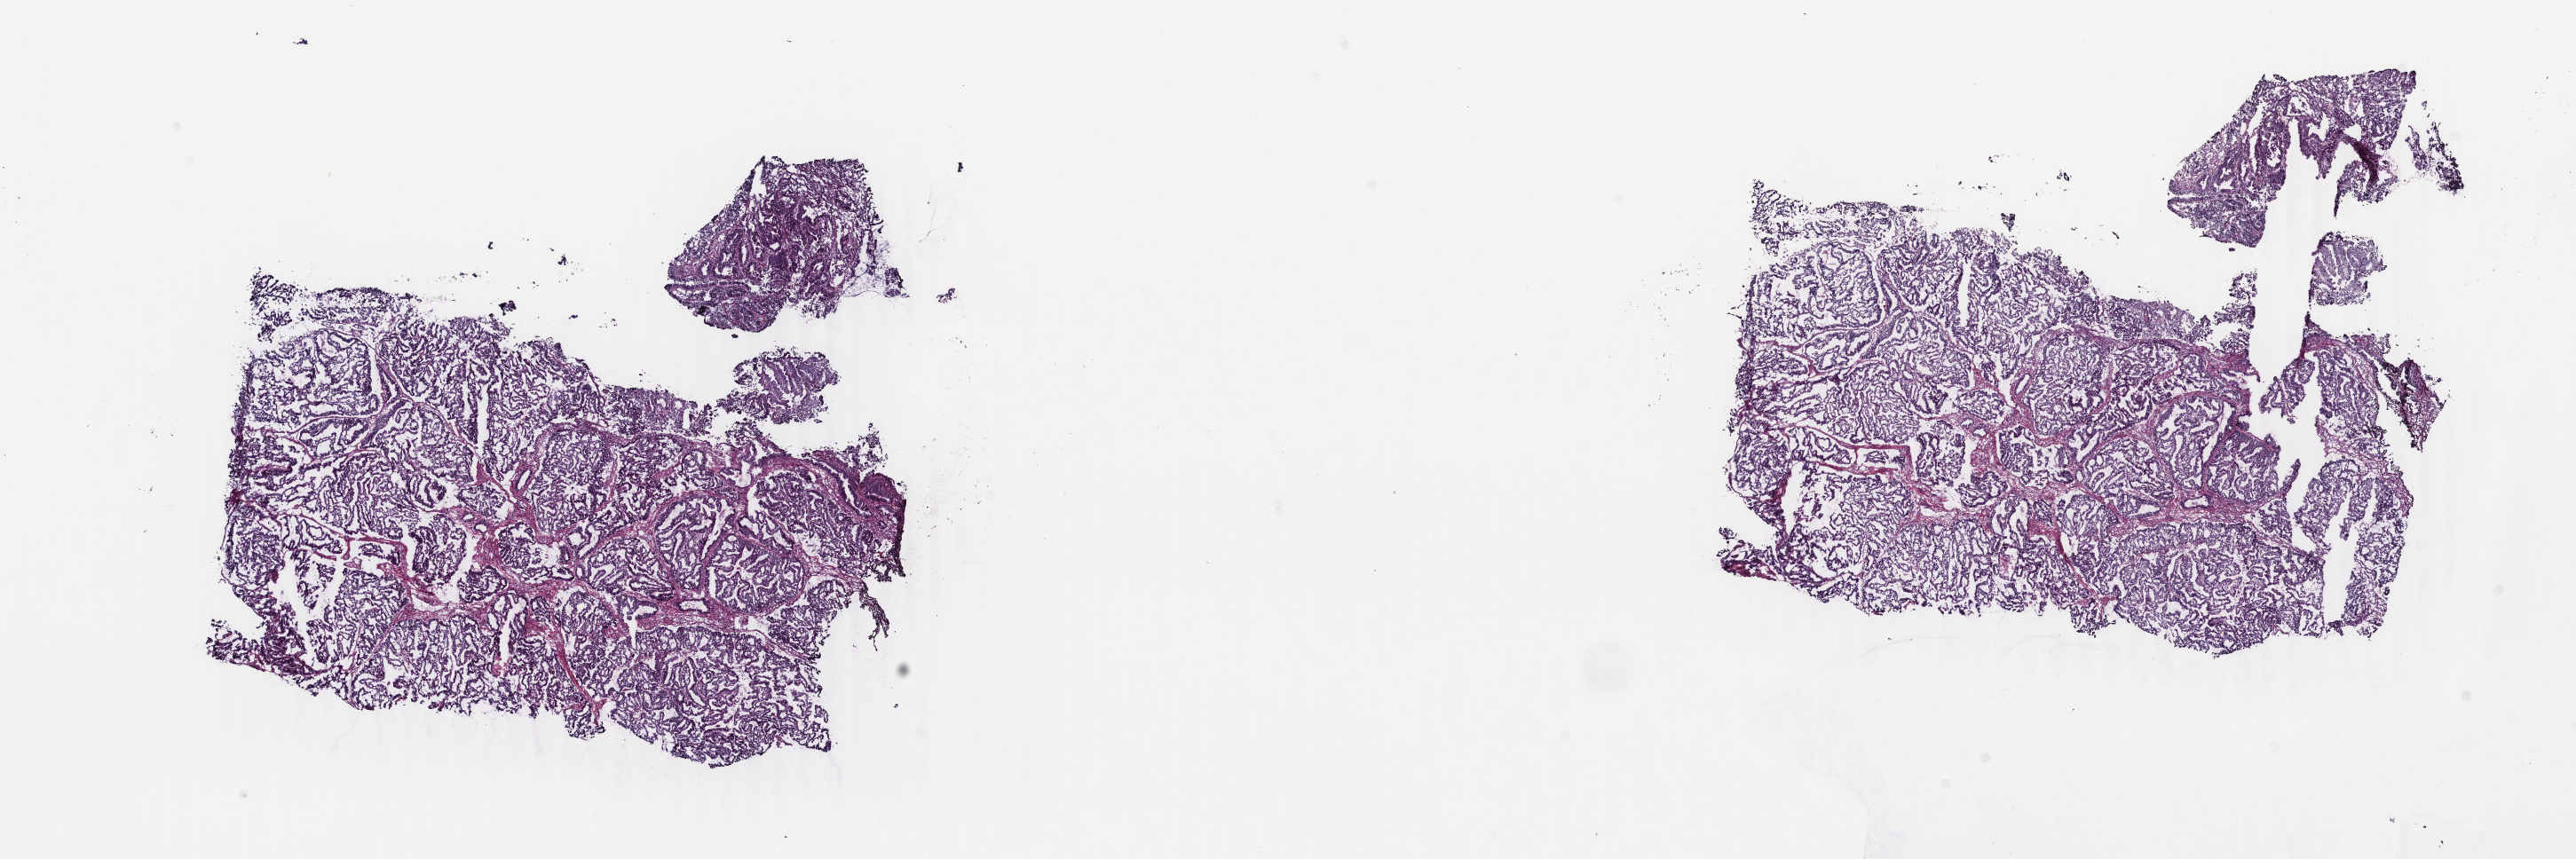
Digitized H&E-stained tissue section (whole slide), whole scanned area (about 23.1 x 7.7 mm) shown as a low-resolution overview, frozen section, sample: primary tumour, uterus. Female, age 61 years at initial diagnosis. Histologic grade: G2 (moderately differentiated). Composition of this section per pathologist review: tumour cells 80%, tumour nuclei 90%, normal cells 10%, stromal cells 0%, necrosis 10%. Inflammatory infiltration, as recorded: lymphocyte infiltration 10%, monocyte infiltration 0%, neutrophil infiltration 0%.
FIGO stage: IB. Diagnosis: Endometrioid adenocarcinoma, NOS (endometrium).